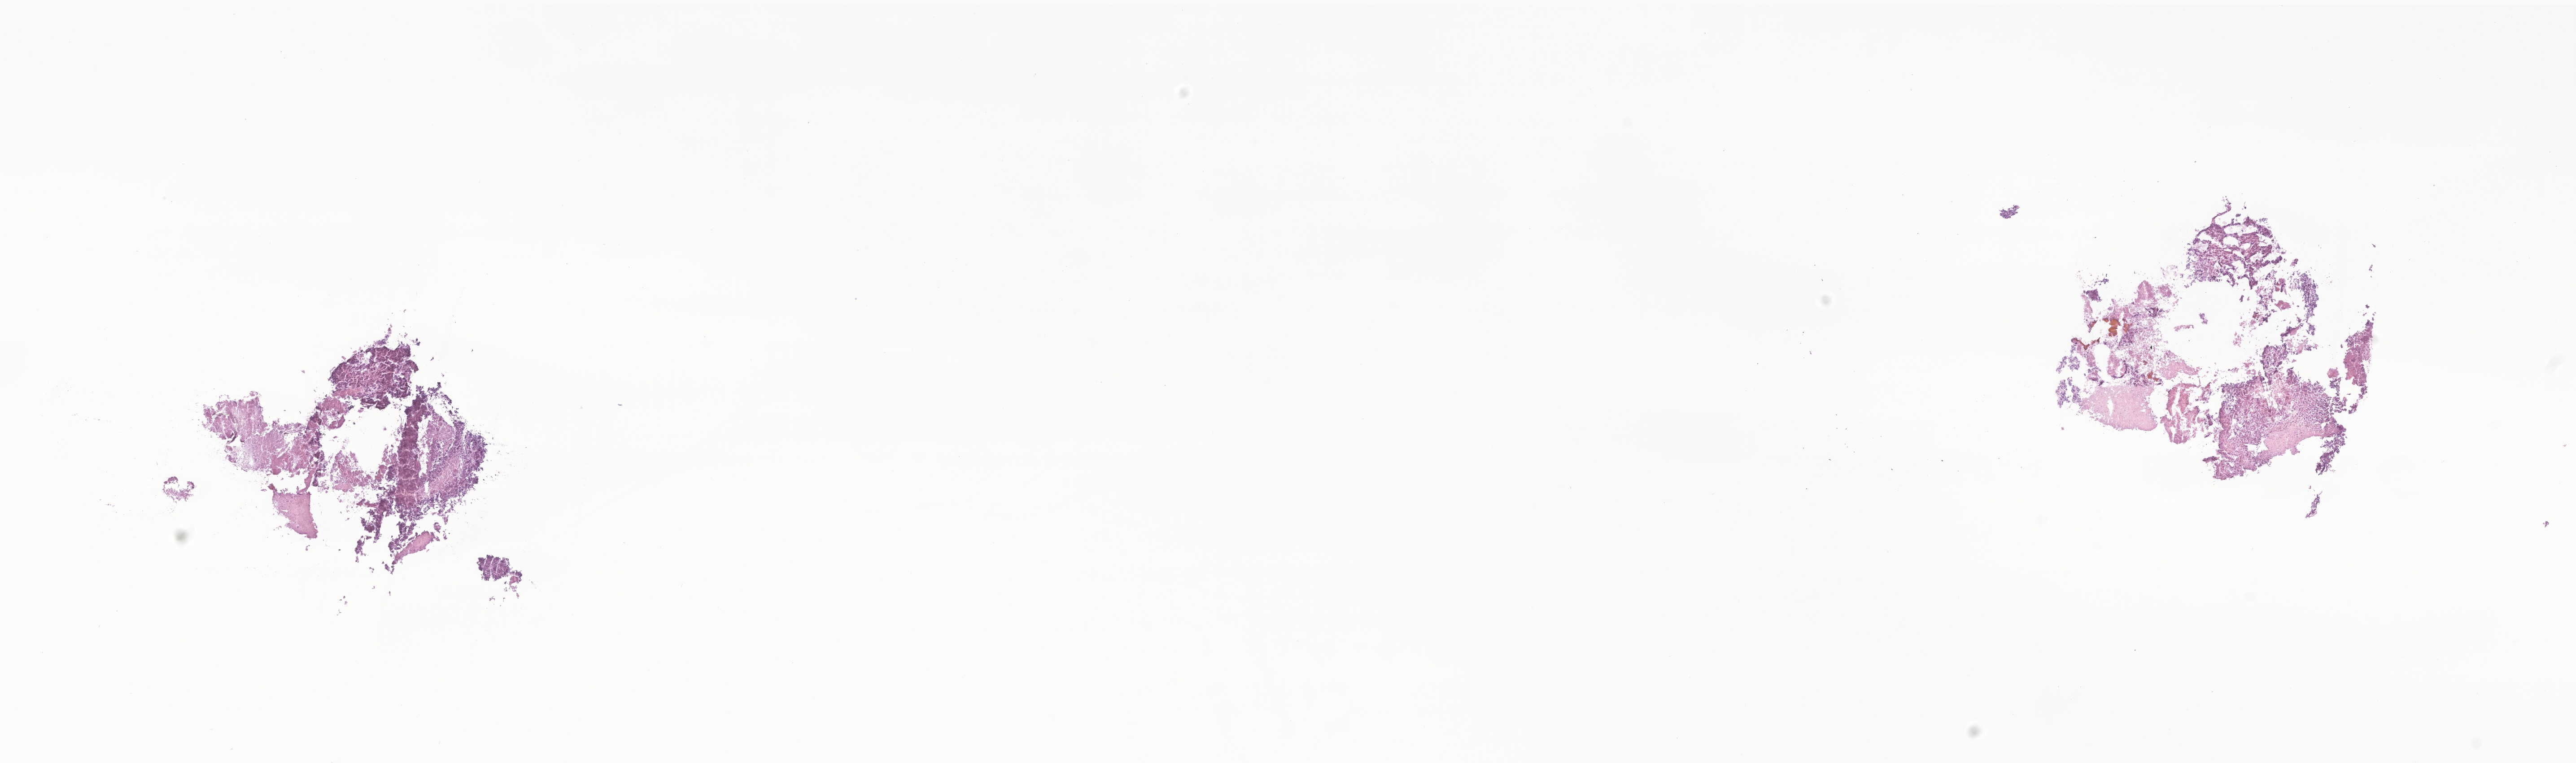
H&E whole-slide image of tumor tissue from the central nervous system — a low-resolution overview of the entire scanned area, about 24.2 x 7.2 mm. Cryosection (OCT / tissue freezing medium). Patient male; age 190 months (15 years 10 months).
Diagnosis: Medulloblastoma, NOS.